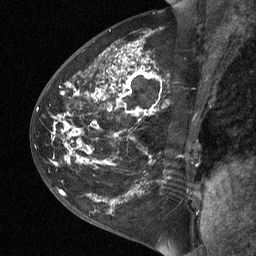
Breast MRI (dynamic contrast-enhanced), one sagittal slice. Slice 28 of 64 in the series (ordered by position). Dynamic contrast-enhanced study with each time point stored as its own series, time point 2 of 3 at this slice position (early post-contrast, ordered by acquisition time). 1.5 T. TE 4.8 ms, TR 27 ms. 2 mm slice thickness. 256 × 256 image matrix, field of view 200 × 200 mm. Patient: female, 42 years. Case-level facts recorded for this patient, not image findings: setting: breast cancer imaged before/during neoadjuvant chemotherapy; receptor status: triple-negative.
Structures marked on this image (semi-automatically segmented with operator editing):
- analysis volume of interest (the breast-tissue region the enhancement analysis was run in; not a lesion): bounding box [x1, y1, x2, y2] px = [43, 29, 202, 190]
- tumour enhancement mask (voxels above the 90 % enhancement threshold inside the analysis volume of interest): [60, 44, 147, 162]